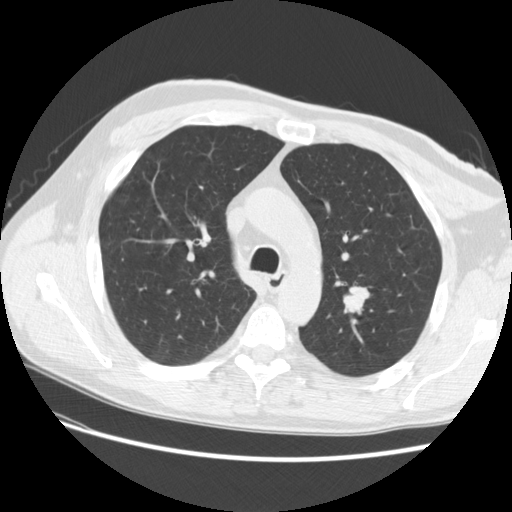
Low-dose screening chest CT, one axial slice. Slice 183 of 256 in the series (ordered by position). 120 kVp. Lung window (W 1500 / L -600 HU). 2.5 mm slice thickness. 512 × 512 image matrix, field of view 366 × 366 mm.
Outlined on this slice (manually delineated by an expert):
- lesion 1 (tumor, upper lobe of left lung): bounding box (x1, y1, x2, y2) in pixels: (344, 287, 369, 312)